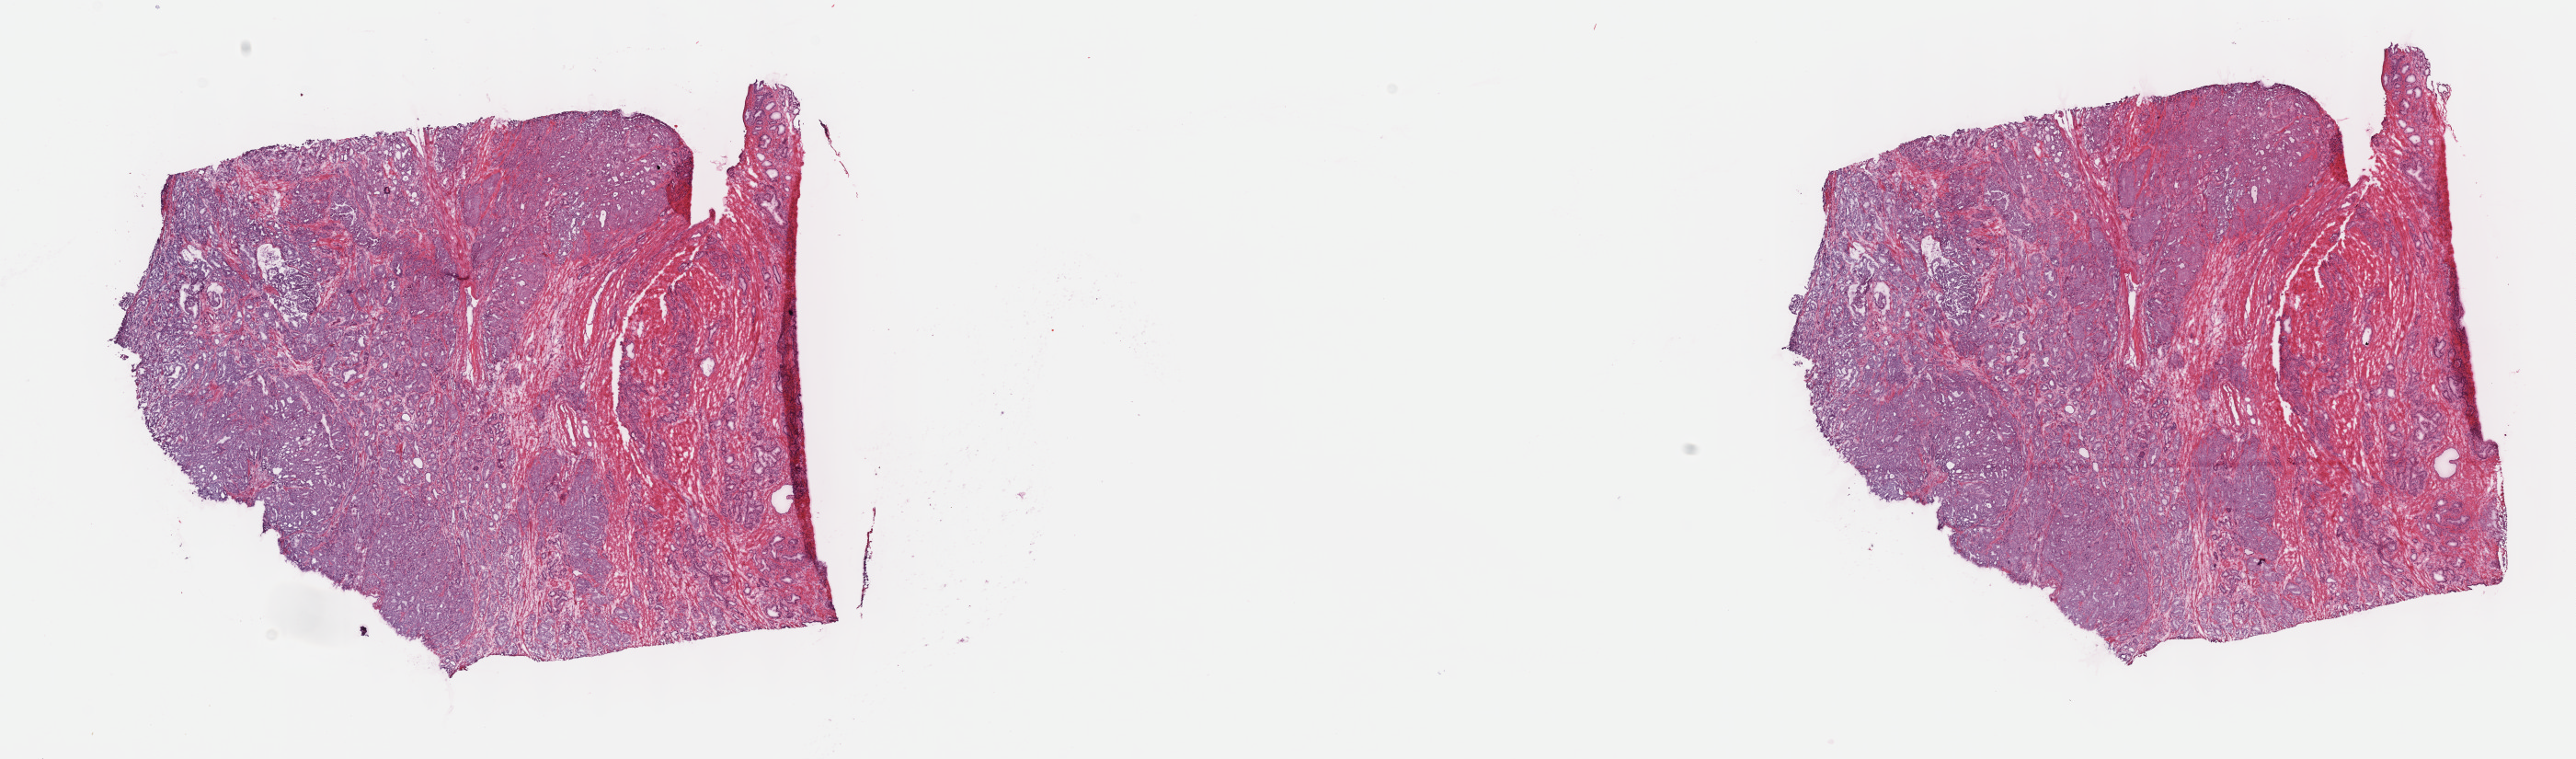
Digitized Hematoxylin and eosin (H&E) stained tissue section (whole slide), shown as a low-resolution overview of the whole scanned area (about 22.7 x 6.7 mm), frozen section from the top of the tissue portion, prostate, primary tumour sample. Male, age 61 years at initial diagnosis. Slide review estimates, as recorded: tumour cells 70%, tumour nuclei 80%.
Histologic diagnosis: Adenocarcinoma, NOS.